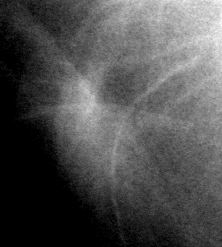
Crop from a digitized film mammogram around one marked abnormality; right breast; MLO view; BI-RADS breast density category 1 (scale 1–4).
Marked abnormality: mass, shape irregular, margins ill defined; BI-RADS assessment category 3; subtlety rating 2 on a 1 (subtle) to 5 (obvious) scale; pathology result (as recorded, not read from the image): malignant.